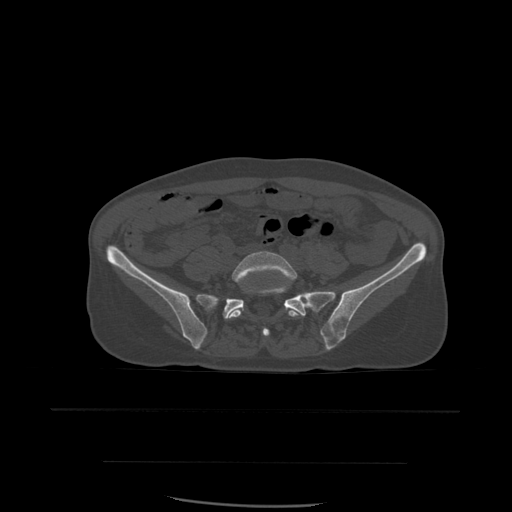
CT including the spine, one axial slice; position 137 of 574 along the scan axis; bone window (W 1800 / L 400 HU); 1.25 mm slice thickness; 512 × 512 image matrix. Patient age 48 years. From the clinical record (not read from this slice): primary cancer: lung; vertebrae with lytic lesions (as recorded): T11.
Structures marked on this image (semi-automatic segmentation, software-assisted and operator-edited):
- L5 vertebra: bounding box [x1, y1, x2, y2] px = [227, 251, 304, 337]